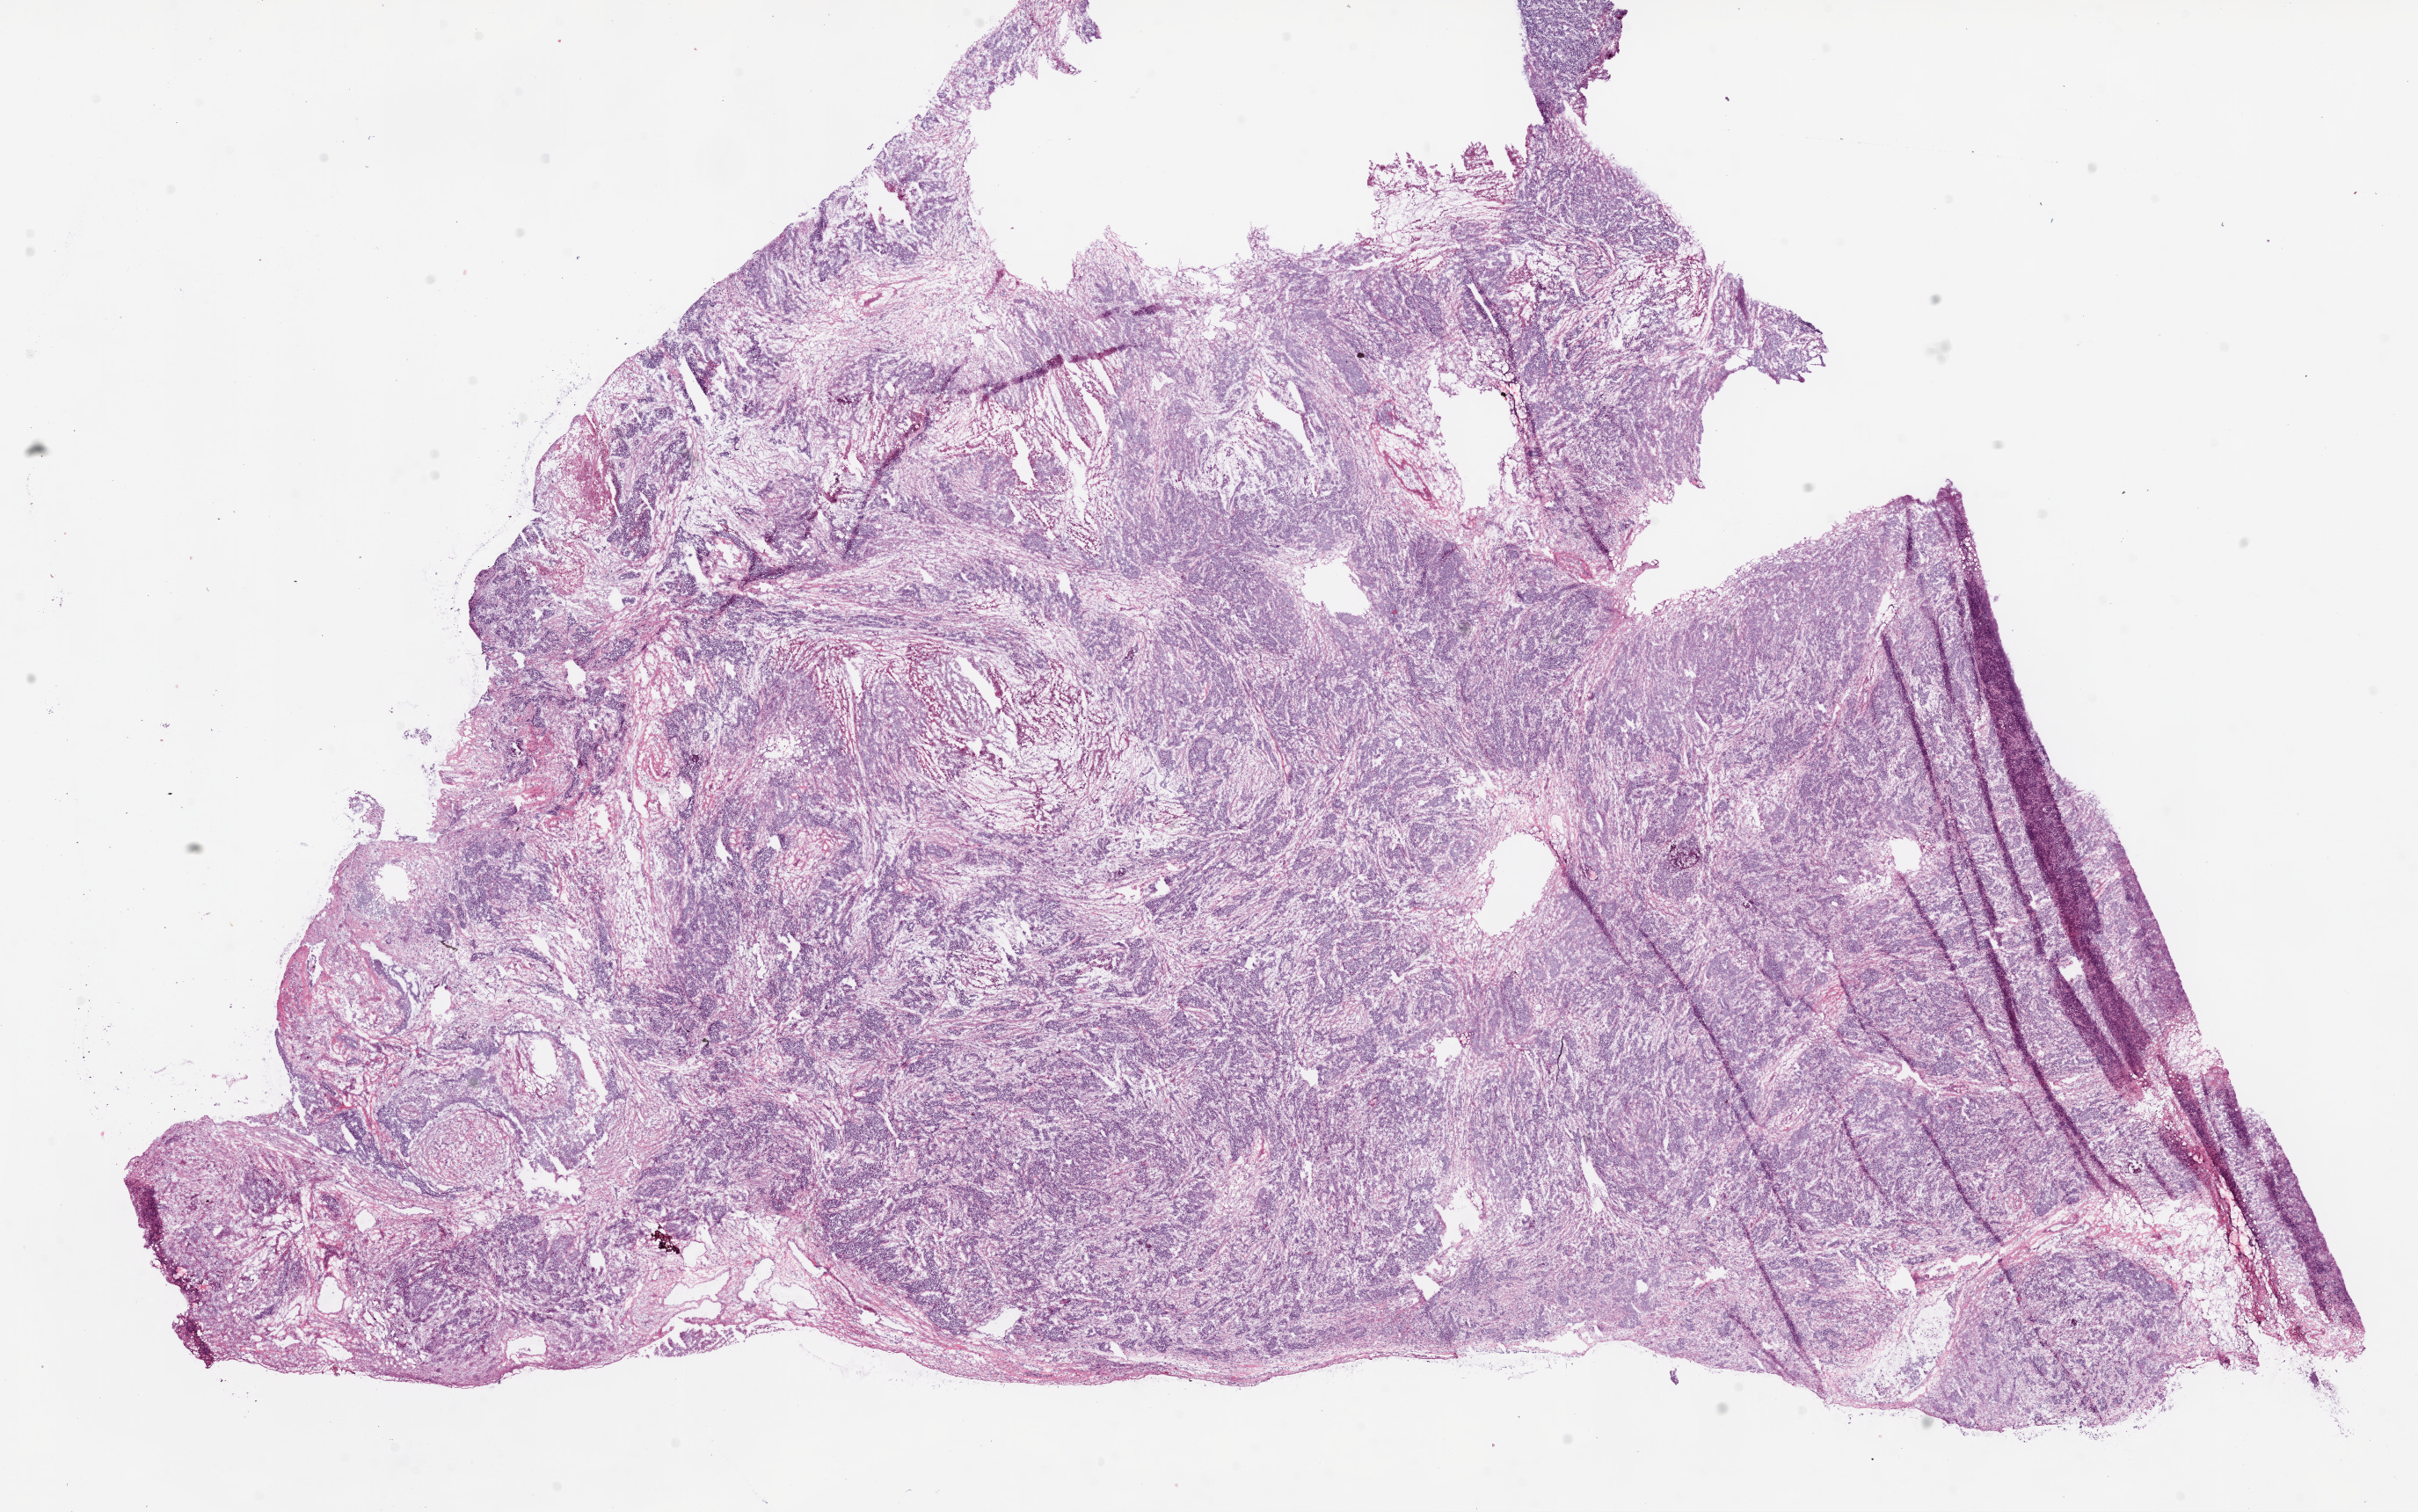
Digitized H&E tissue section (whole slide) — a low-resolution overview of the entire scanned area, about 22.1 x 13.8 mm. Frozen section from the top of the tissue portion. Sample: primary tumour, ovary. Female patient; age at initial diagnosis 63 years. Histologic grade: G3 (poorly differentiated). Pathologist review of this section (percent, as recorded): tumour cells 60%, tumour nuclei 80%, normal cells 0%, stromal cells 30%, necrosis 10%.
• FIGO stage: IIIC
• histologic diagnosis: Serous cystadenocarcinoma, NOS